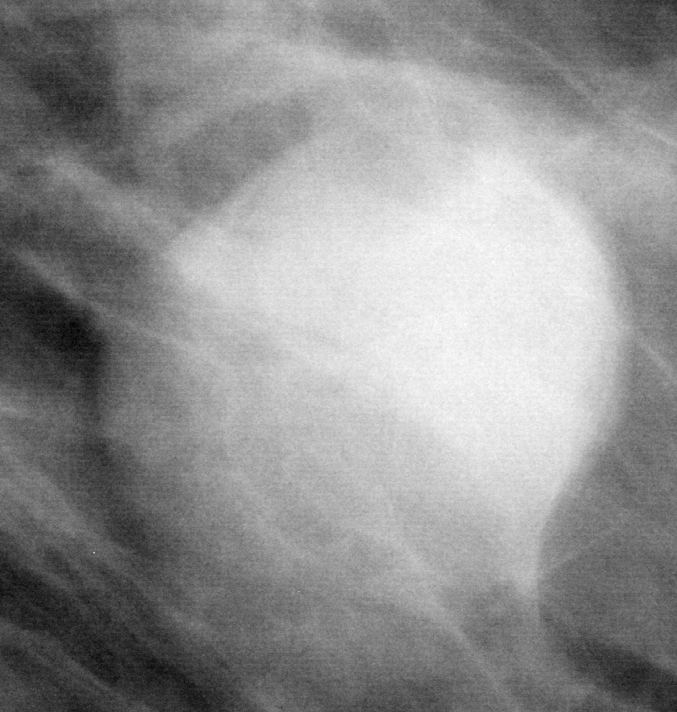
Cropped region of a digitized screen-film mammogram centred on a radiologist-marked abnormality; left breast; MLO view; BI-RADS breast density category 2 (scale 1–4).
- Mass, shape round, margins obscured; BI-RADS assessment category 4; subtlety rating 5 on a 1 (subtle) to 5 (obvious) scale; pathology (as recorded): benign.